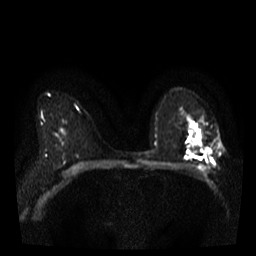
Breast MRI, one axial slice. Slice 24 of 38 in the series (ordered by position). Diffusion-weighted series; image 2 of 4 stored at this slice position (different b-values; order by instance number). 3 T. 5 mm slice thickness. 256 × 256 image matrix, field of view 320 × 320 mm. Female patient.
Outlined on this slice (outlined manually by an expert reader):
- tumour on diffusion-weighted imaging: bounding box [x1, y1, x2, y2] px = [205, 148, 212, 154]